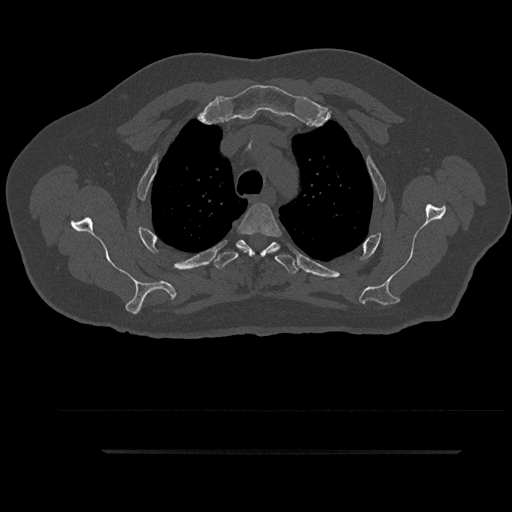
CT including the spine, one axial slice; position 698 of 797 along the scan axis; reconstruction kernel Br40s/3; 120 kVp; bone window (W 1800 / L 400 HU); 0.5 mm slice thickness; 512 × 512 image matrix, field of view 432 × 432 mm. Male patient, age 63 years. From the clinical record (not read from this slice): primary cancer: renal; vertebrae with lytic lesions (as recorded): T8.
Outlined on this slice (semi-automatically segmented with operator editing):
- T3 vertebra: box from (x=238, y=202) to (x=281, y=255) px
- T4 vertebra: (x=211, y=239)–(x=299, y=274)